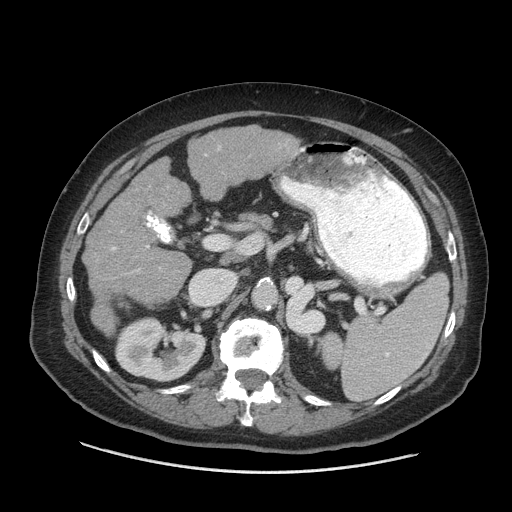
Contrast-enhanced abdominal CT (liver protocol), one axial slice. Position 31 of 77 along the scan axis. Soft-tissue window (W 400 / L 40 HU). 2.5 mm slice thickness. 512 × 512 image matrix, field of view 420 × 420 mm. Case-level facts recorded for this patient, not image findings: diagnosis: hepatocellular carcinoma (patient treated with transarterial chemoembolisation; whether this scan precedes or follows treatment is not stated here); TNM stage (as recorded): Stage-I; Child-Pugh class: A; tumour nodularity: uninodular.
Structures marked on this image (semi-automatic segmentation, software-assisted and operator-edited):
- liver parenchyma outside the tumour (the mass and vessels are separate outlines, so this box may not span the whole liver): box from (x=84, y=126) to (x=301, y=292) px
- liver vessels: (x=112, y=211)–(x=152, y=271)